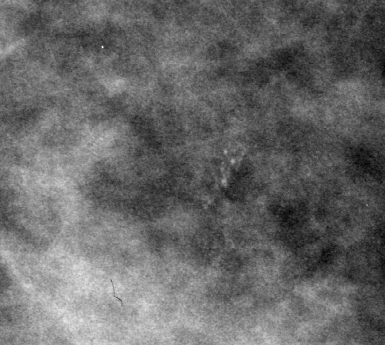
Region of interest cut from a scanned film mammogram (one marked finding); left breast; CC view.
Calcifications, morphology amorphous, distribution clustered; BI-RADS assessment category 3; subtlety rating 2 on a 1 (subtle) to 5 (obvious) scale; pathology result (as recorded, not read from the image): benign.